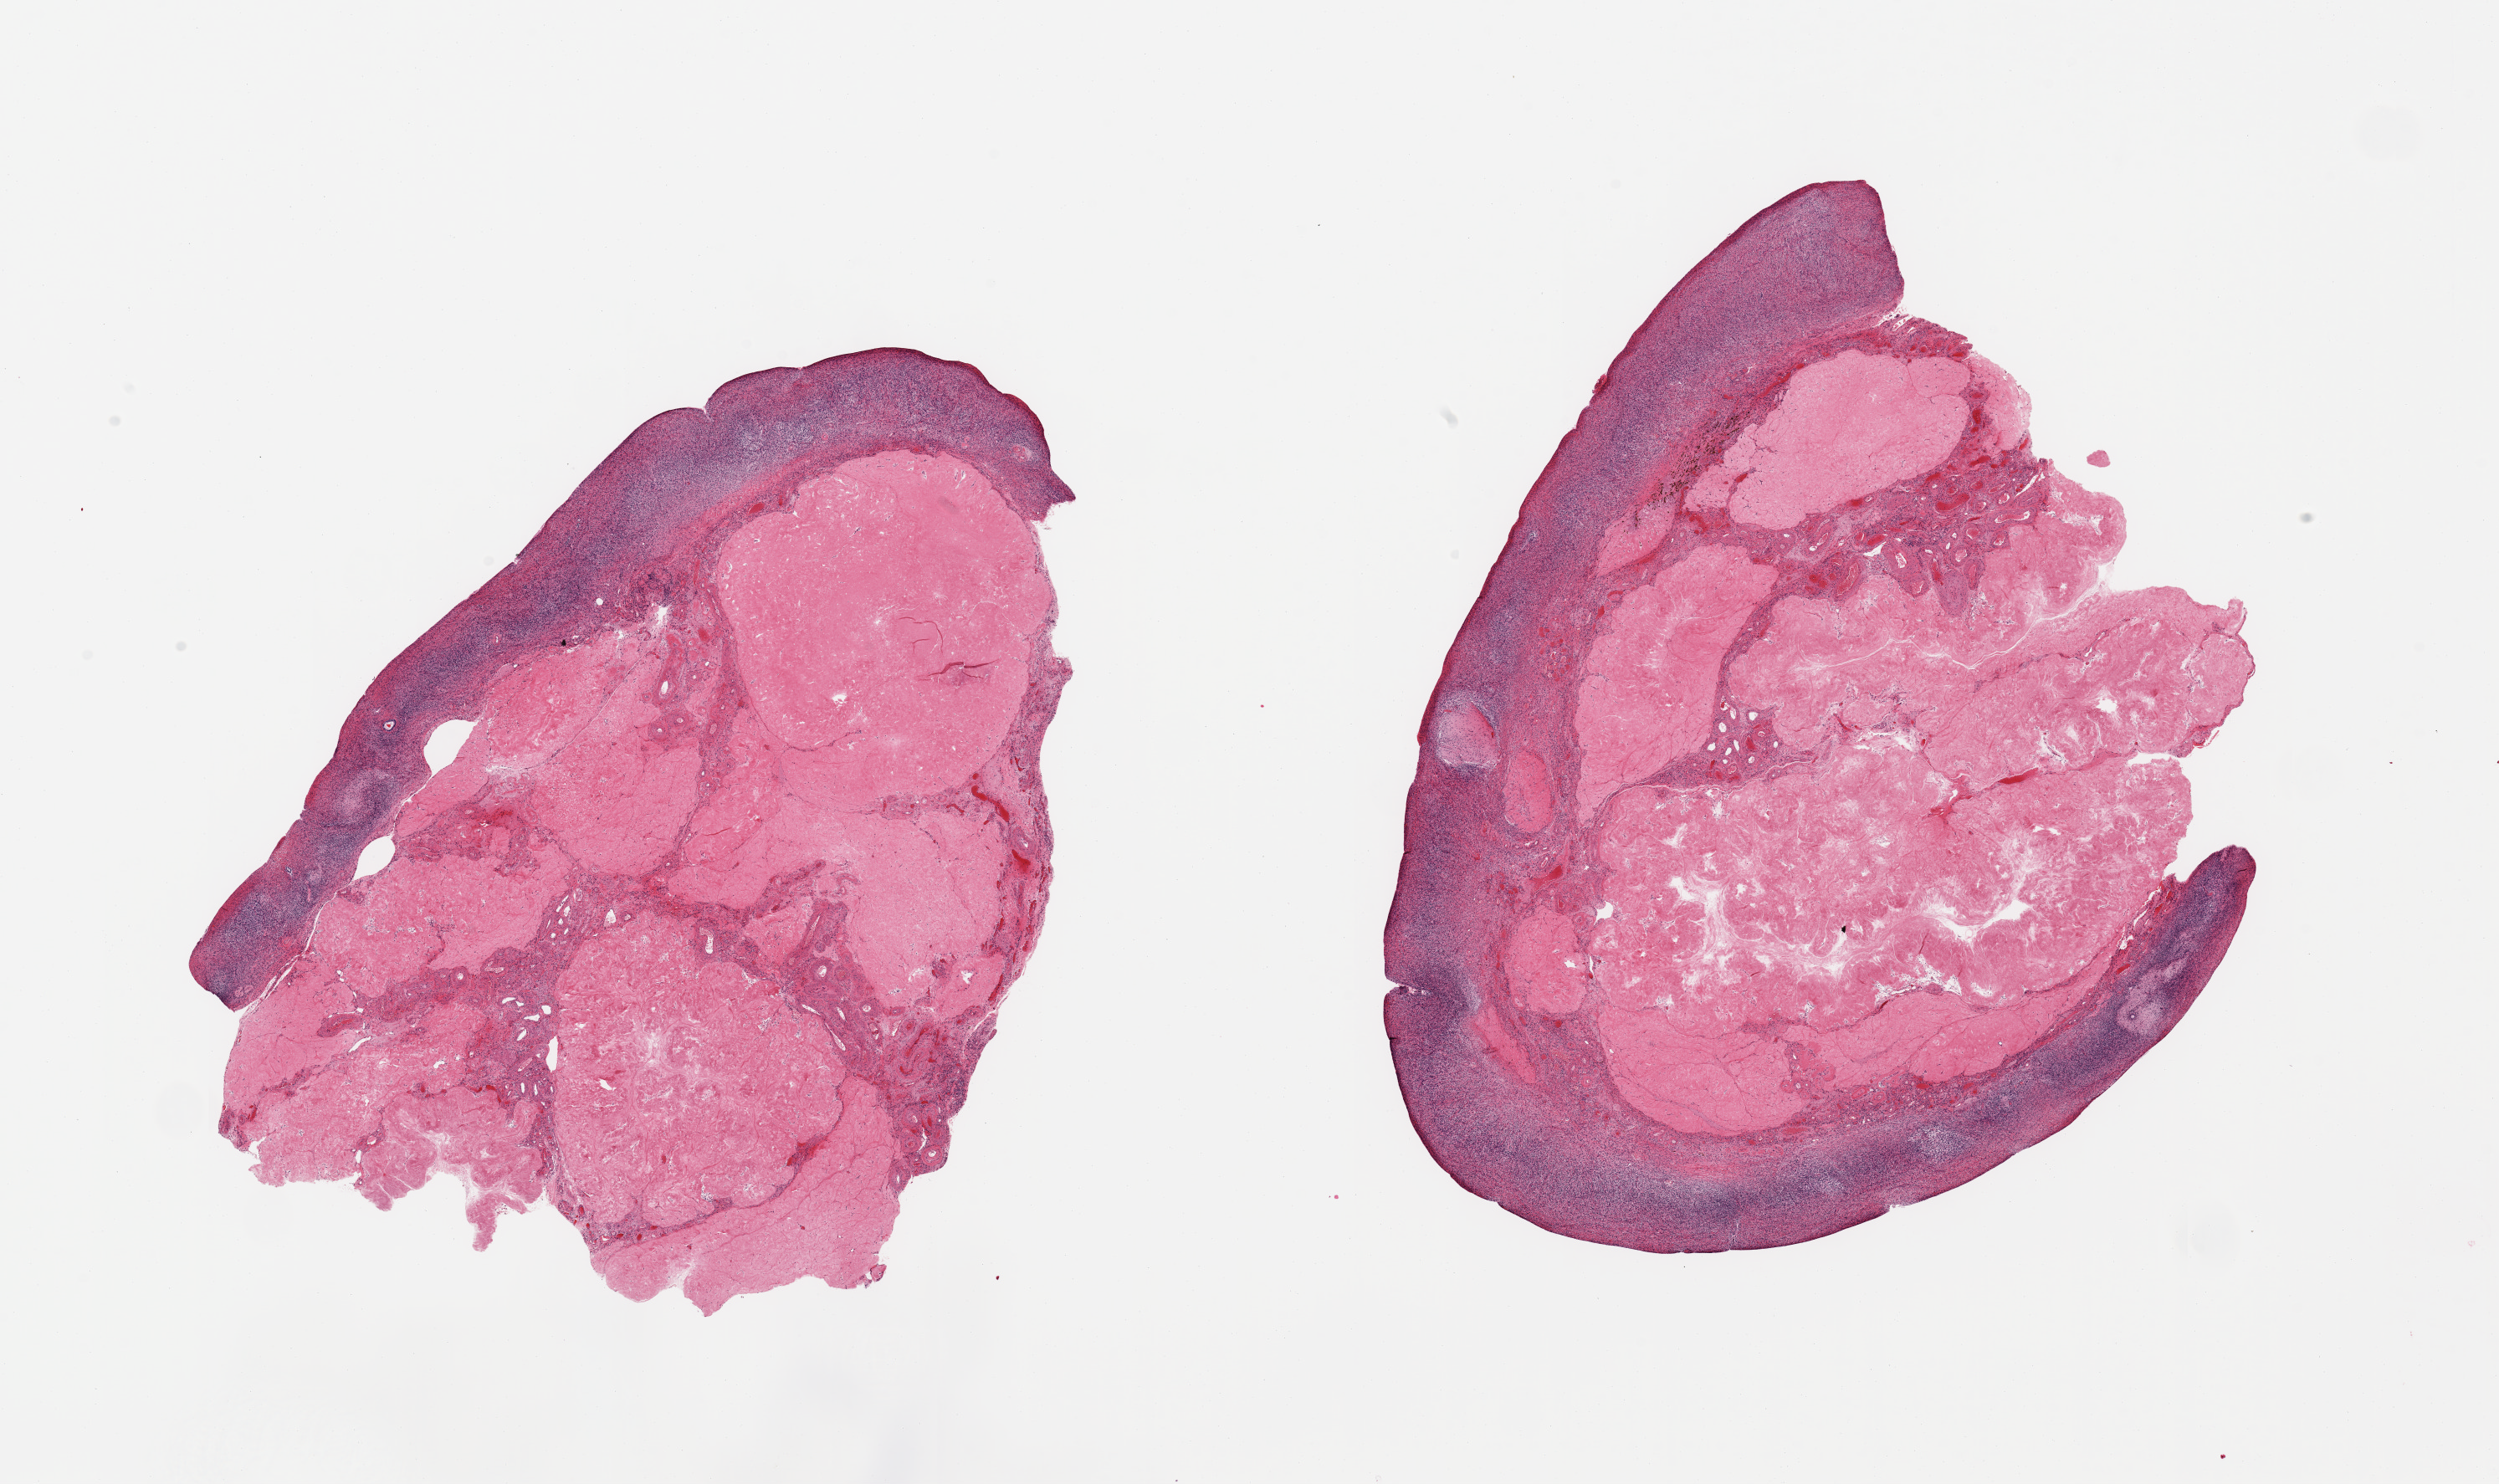
Digitized haematoxylin and eosin-stained section — a low-resolution overview of the entire scanned area, about 23.6 x 14.0 mm; PAXgene-fixed, paraffin-embedded tissue; target tissue: ovary; donor tissue sample. Donor: female.
Reviewer comment on this tissue sample: 2 pieces, post menopausal atrophy.